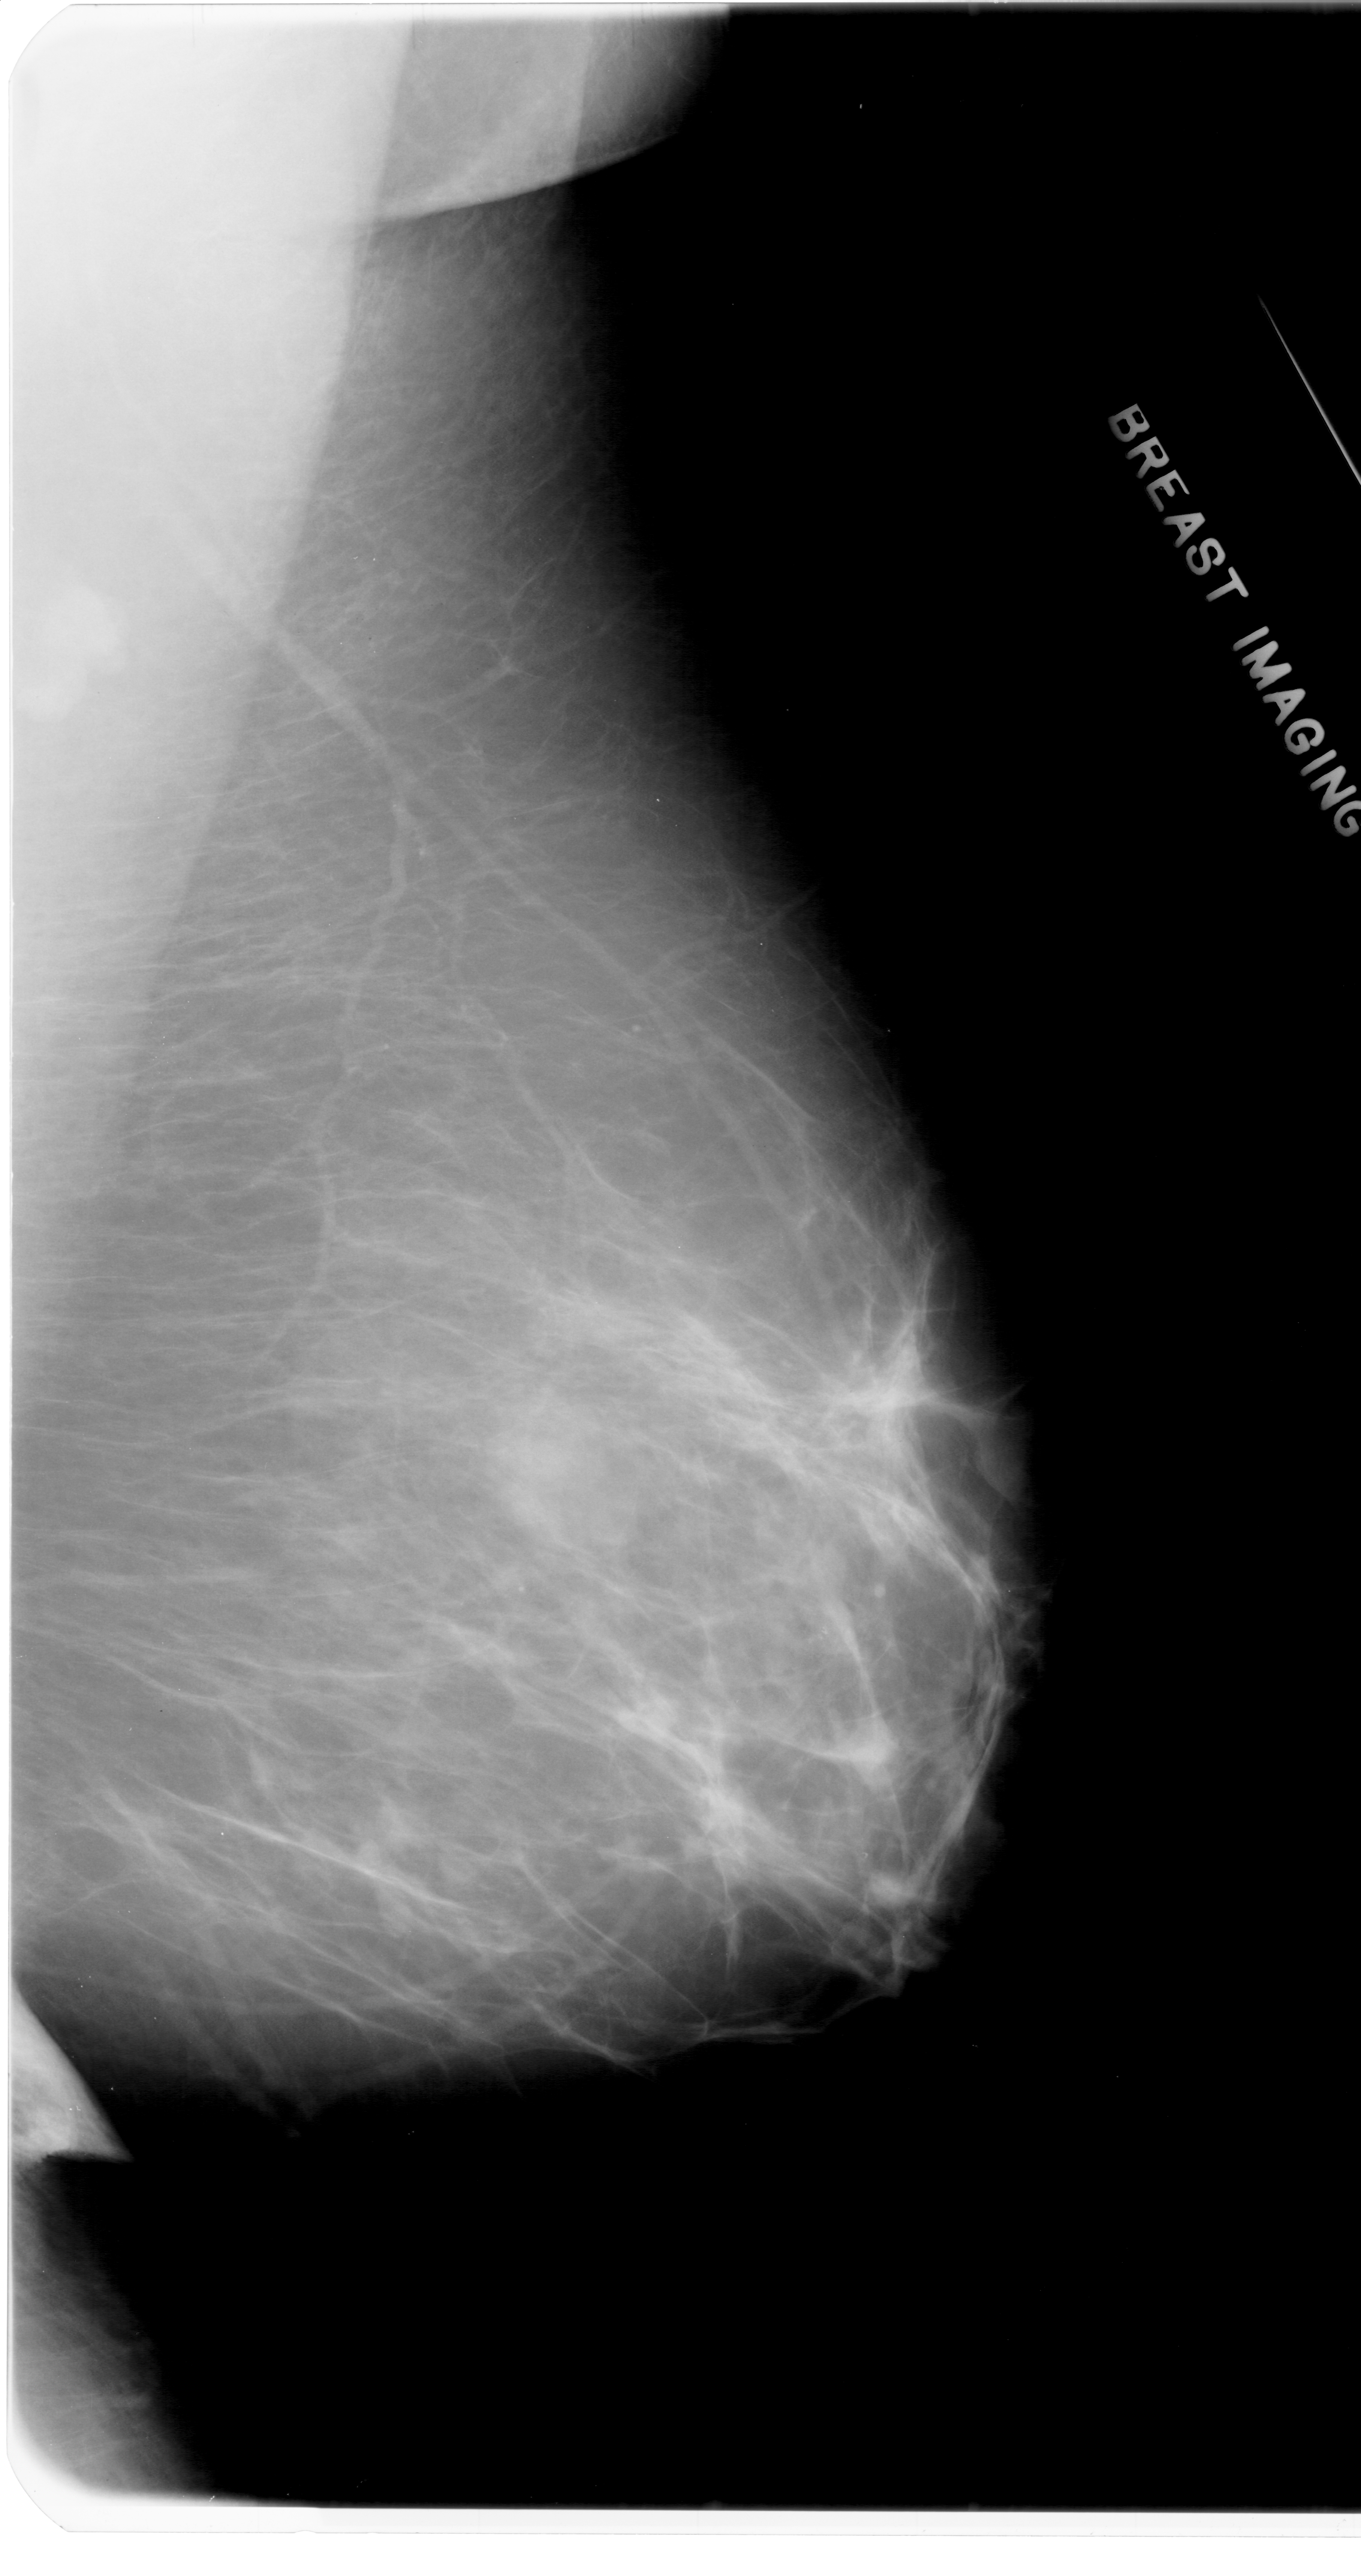
Digitized screen-film mammogram. Right breast. Mediolateral oblique (MLO) view. Breast composition: scattered fibroglandular densities (BI-RADS density category 2 of 4). 1361 × 2576 image matrix.
Expert-marked regions of interest on this film, with their recorded descriptors:
- calcifications, morphology pleomorphic, distribution clustered; BI-RADS assessment category 4; pathology (as recorded): benign: bounding box [x1, y1, x2, y2] px = [781, 1624, 836, 1667]